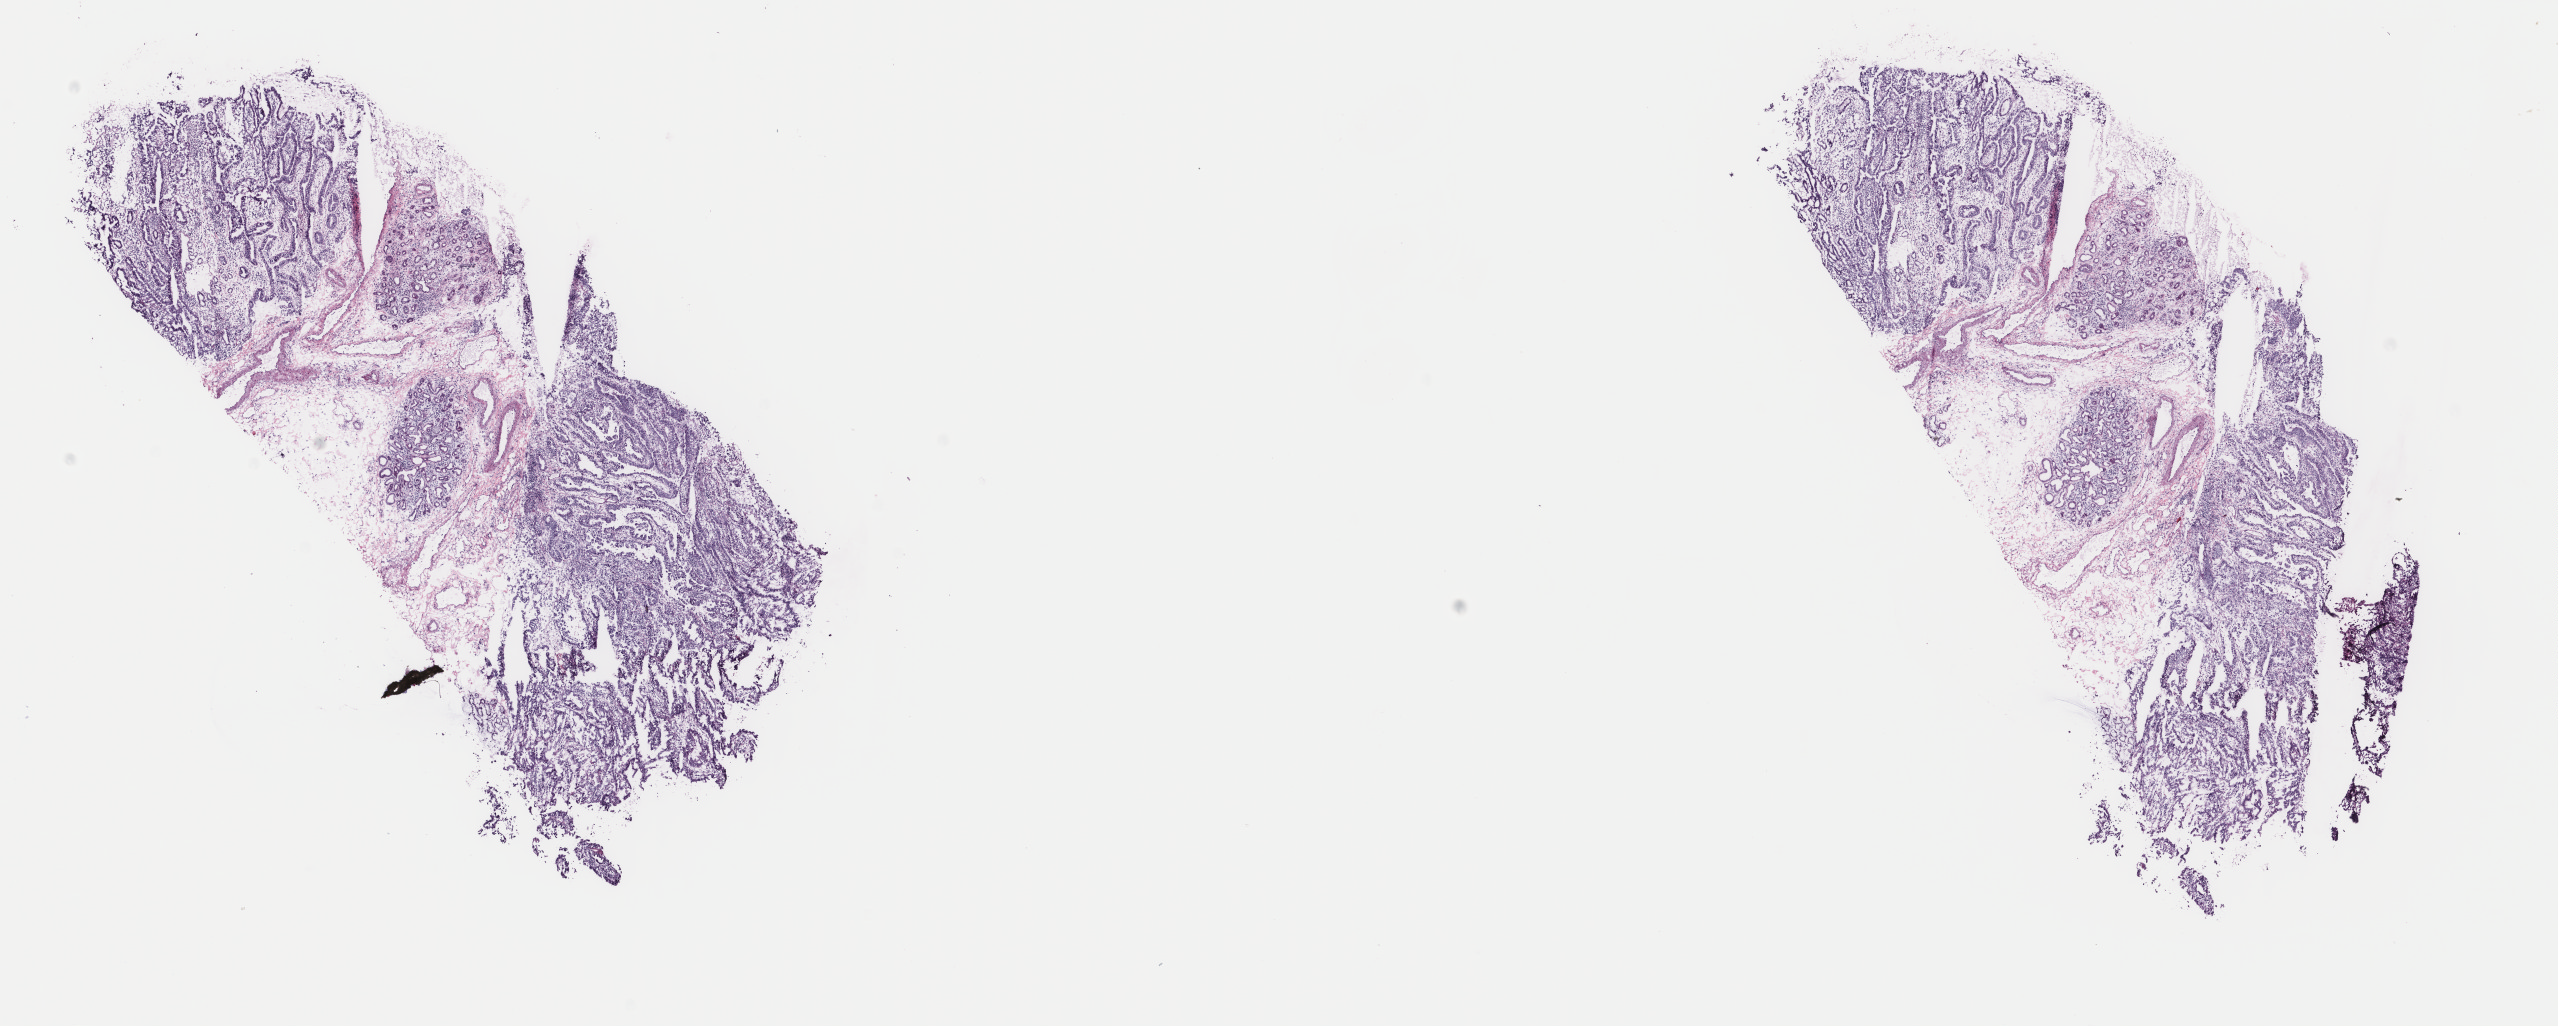
Whole-slide histology image, H&E — low-resolution overview of the scanned area, about 20.3 x 8.1 mm; frozen section from the top of the tissue portion; stomach, primary tumour sample. Patient: male, age at initial diagnosis 84 years. Histologic grade: G2 (moderately differentiated). Composition of this section per pathologist review: tumour cells 70%, tumour nuclei 65%, normal cells 30%, stromal cells 0%, necrosis 0%. Inflammatory infiltration, as recorded: lymphocyte infiltration 5%, monocyte infiltration 0%, neutrophil infiltration 0%.
Pathologic diagnosis: Adenocarcinoma, NOS (cardia, NOS).